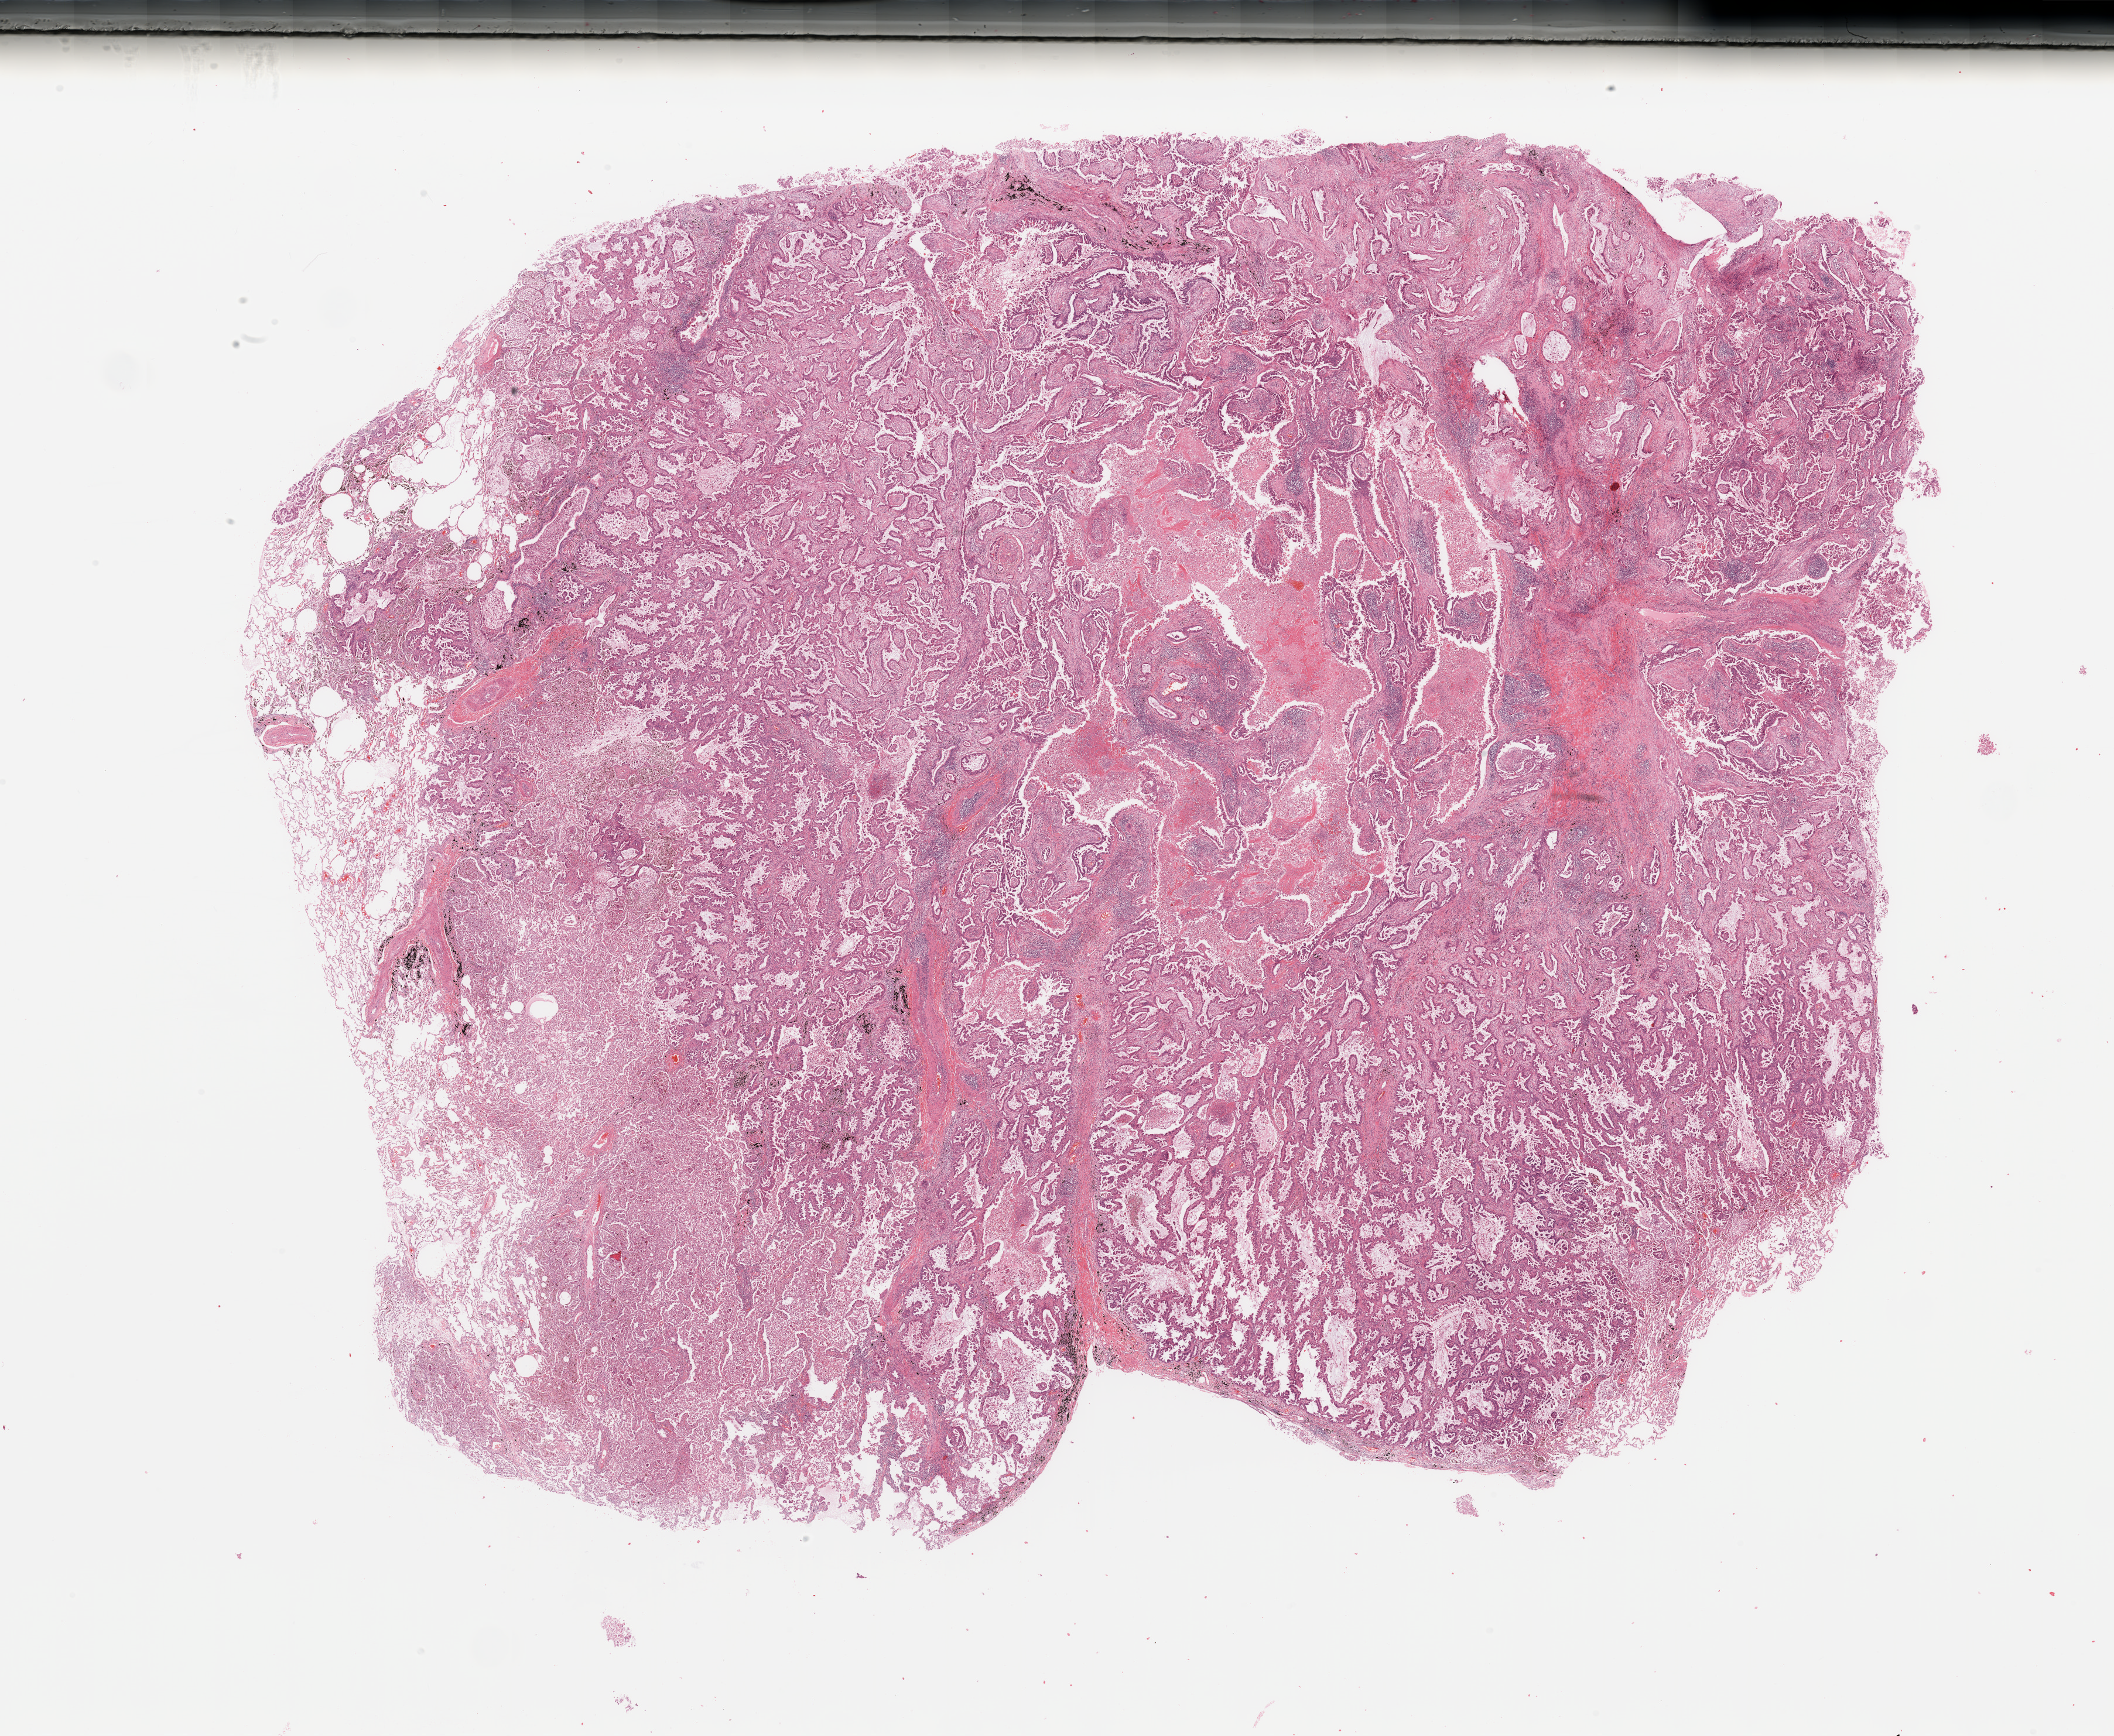
H&E-stained whole-slide image, a low-resolution overview of the entire scanned area, about 28.5 x 23.4 mm (acquisition: 20x scan), tumour tissue sample, sampled site: lung. Male, 58 y/o. Histologic grade: G2 (moderately differentiated). Pathologist review of this section (percent, as recorded): tumour nuclei 70%, necrosis 15%.
Histologic diagnosis: Adenocarcinoma, NOS. AJCC pathologic stage: IIIA.